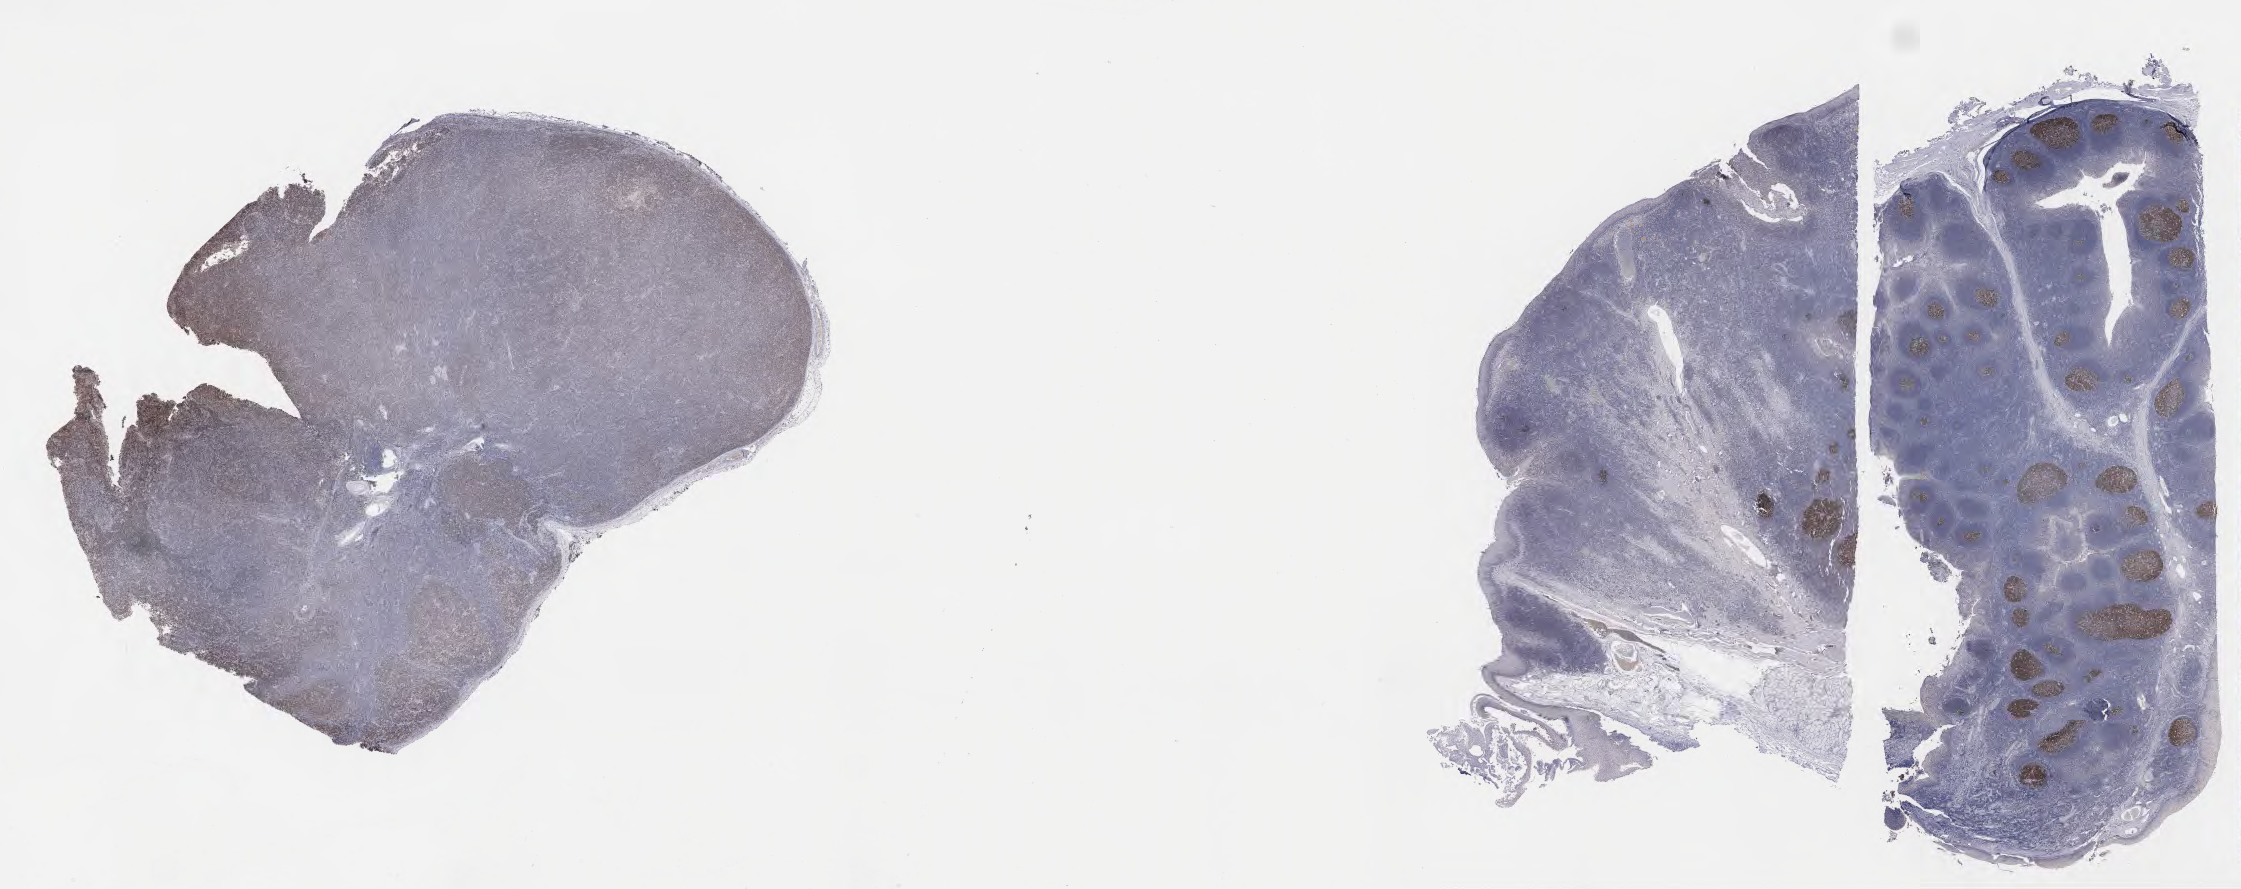
Immunohistochemistry (IHC) whole-slide image stained for BCL6 — a low-resolution overview of the entire scanned area, about 36.2 x 14.4 mm, tumor tissue, site: lymph node. Male patient, aged 32.
* histologic diagnosis: Diffuse large B-cell lymphoma, NOS